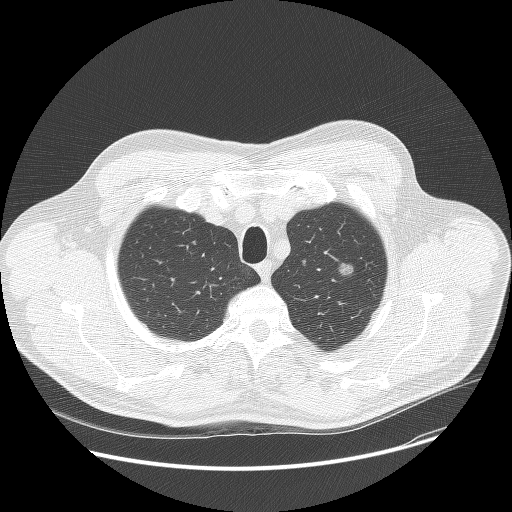
Axial slice from a low-dose chest CT screening exam. First (baseline) screen. Lung window (W 1500 / L -600 HU). Slice 19 of 132 in the series. 512 × 512 image matrix, field of view 400 × 400 mm. Male participant, aged 60 years at enrolment. Former smoker at enrolment.
Lesion marked by an expert reader, bounding box <325,248,371,291> (left, top, right, bottom; pixels). The screening reader recorded 2 non-calcified nodules or masses ≥4 mm on this exam (left upper lobe, right lower lobe); which of them this box marks is not recorded. Official screen result: positive, change unspecified: nodule(s) >= 4 mm or enlarging nodule(s), mass(es), or other non-specific abnormalities suspicious for lung cancer. Lung cancer was diagnosed 784 days after this screen: bronchiolo-alveolar carcinoma, non-mucinous, left upper lobe, well differentiated (G1), stage IA (AJCC 6th edition), 16 mm at pathology.